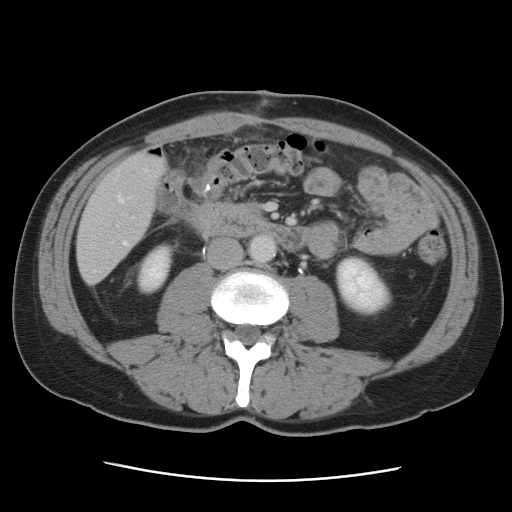
Contrast-enhanced abdominal CT, one axial slice. Slice 19 of 89 in the series (ordered by position). Intravenous contrast given. Soft-tissue window (W 400 / L 40 HU). 512 × 512 image matrix. Male patient, age 59 years. Case-level facts recorded for this patient, not image findings: diagnosis: colorectal cancer liver metastases, imaged before liver resection; multiple liver metastases: yes.
Structures marked on this image (outlined manually by an expert reader):
- hepatic veins: bounding box (x1, y1, x2, y2) in pixels: (94, 169, 147, 272)
- liver: (78, 151, 166, 283)
- planned liver remnant (the part of the liver to remain after resection): (78, 151, 166, 255)